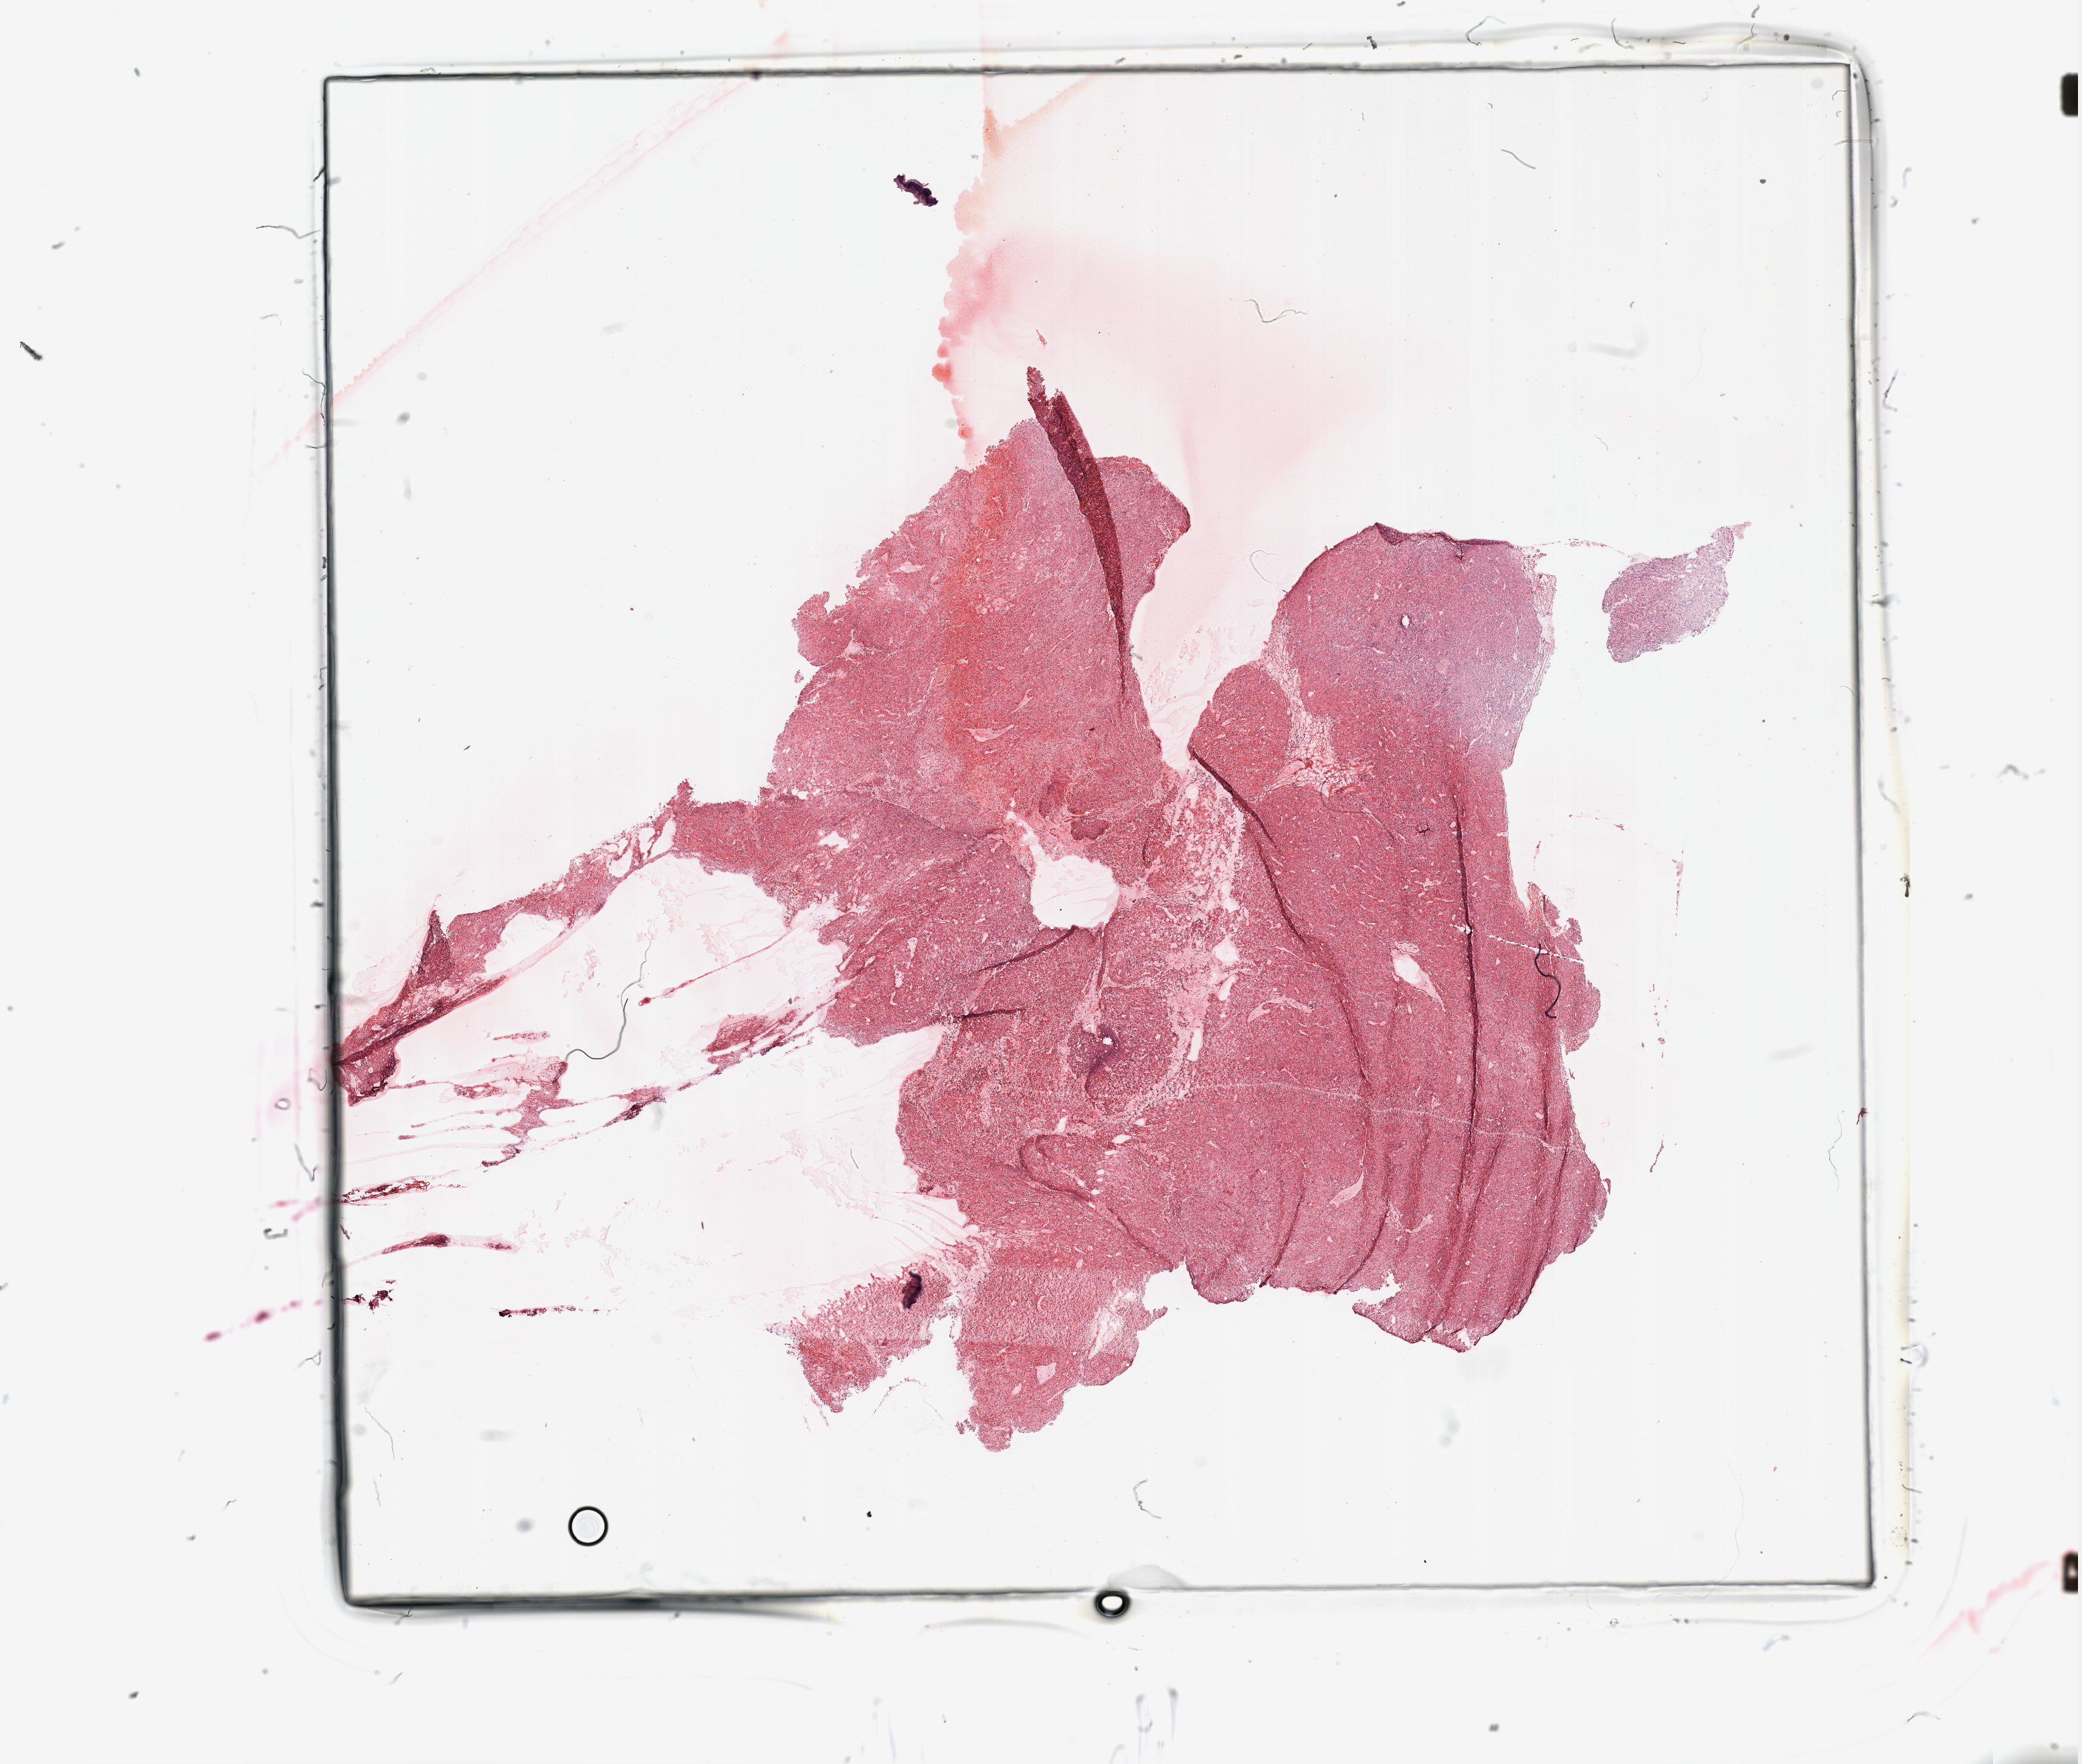
H&E whole-slide image — shown as a low-resolution overview of the whole scanned area (about 24.6 x 20.9 mm); tumour tissue sample, sampled site: kidney. Male, 62 y/o. Histologic grade: G3 (poorly differentiated). Pathologist review of this section (percent, as recorded): tumour nuclei 90%, necrosis 5%.
Diagnosis: Renal cell carcinoma, NOS. AJCC pathologic stage: III.